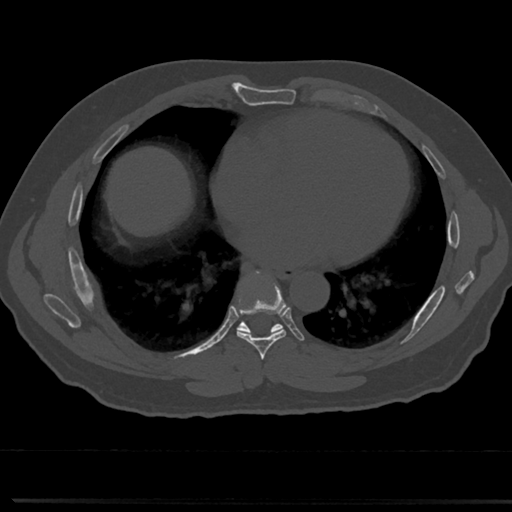
CT including the spine, one axial slice. Reconstruction kernel Br40s/3. Bone window (W 1800 / L 400 HU). 0.5 mm slice thickness. 512 × 512 image matrix, field of view 355 × 355 mm. Male patient, age 61 years. Case-level facts recorded for this patient, not image findings: primary cancer: prostate.
Outlined on this slice (semi-automatically segmented with operator editing):
- T6 vertebra: box from (x=260, y=364) to (x=269, y=377) px
- T7 vertebra: (x=221, y=274)–(x=309, y=355)